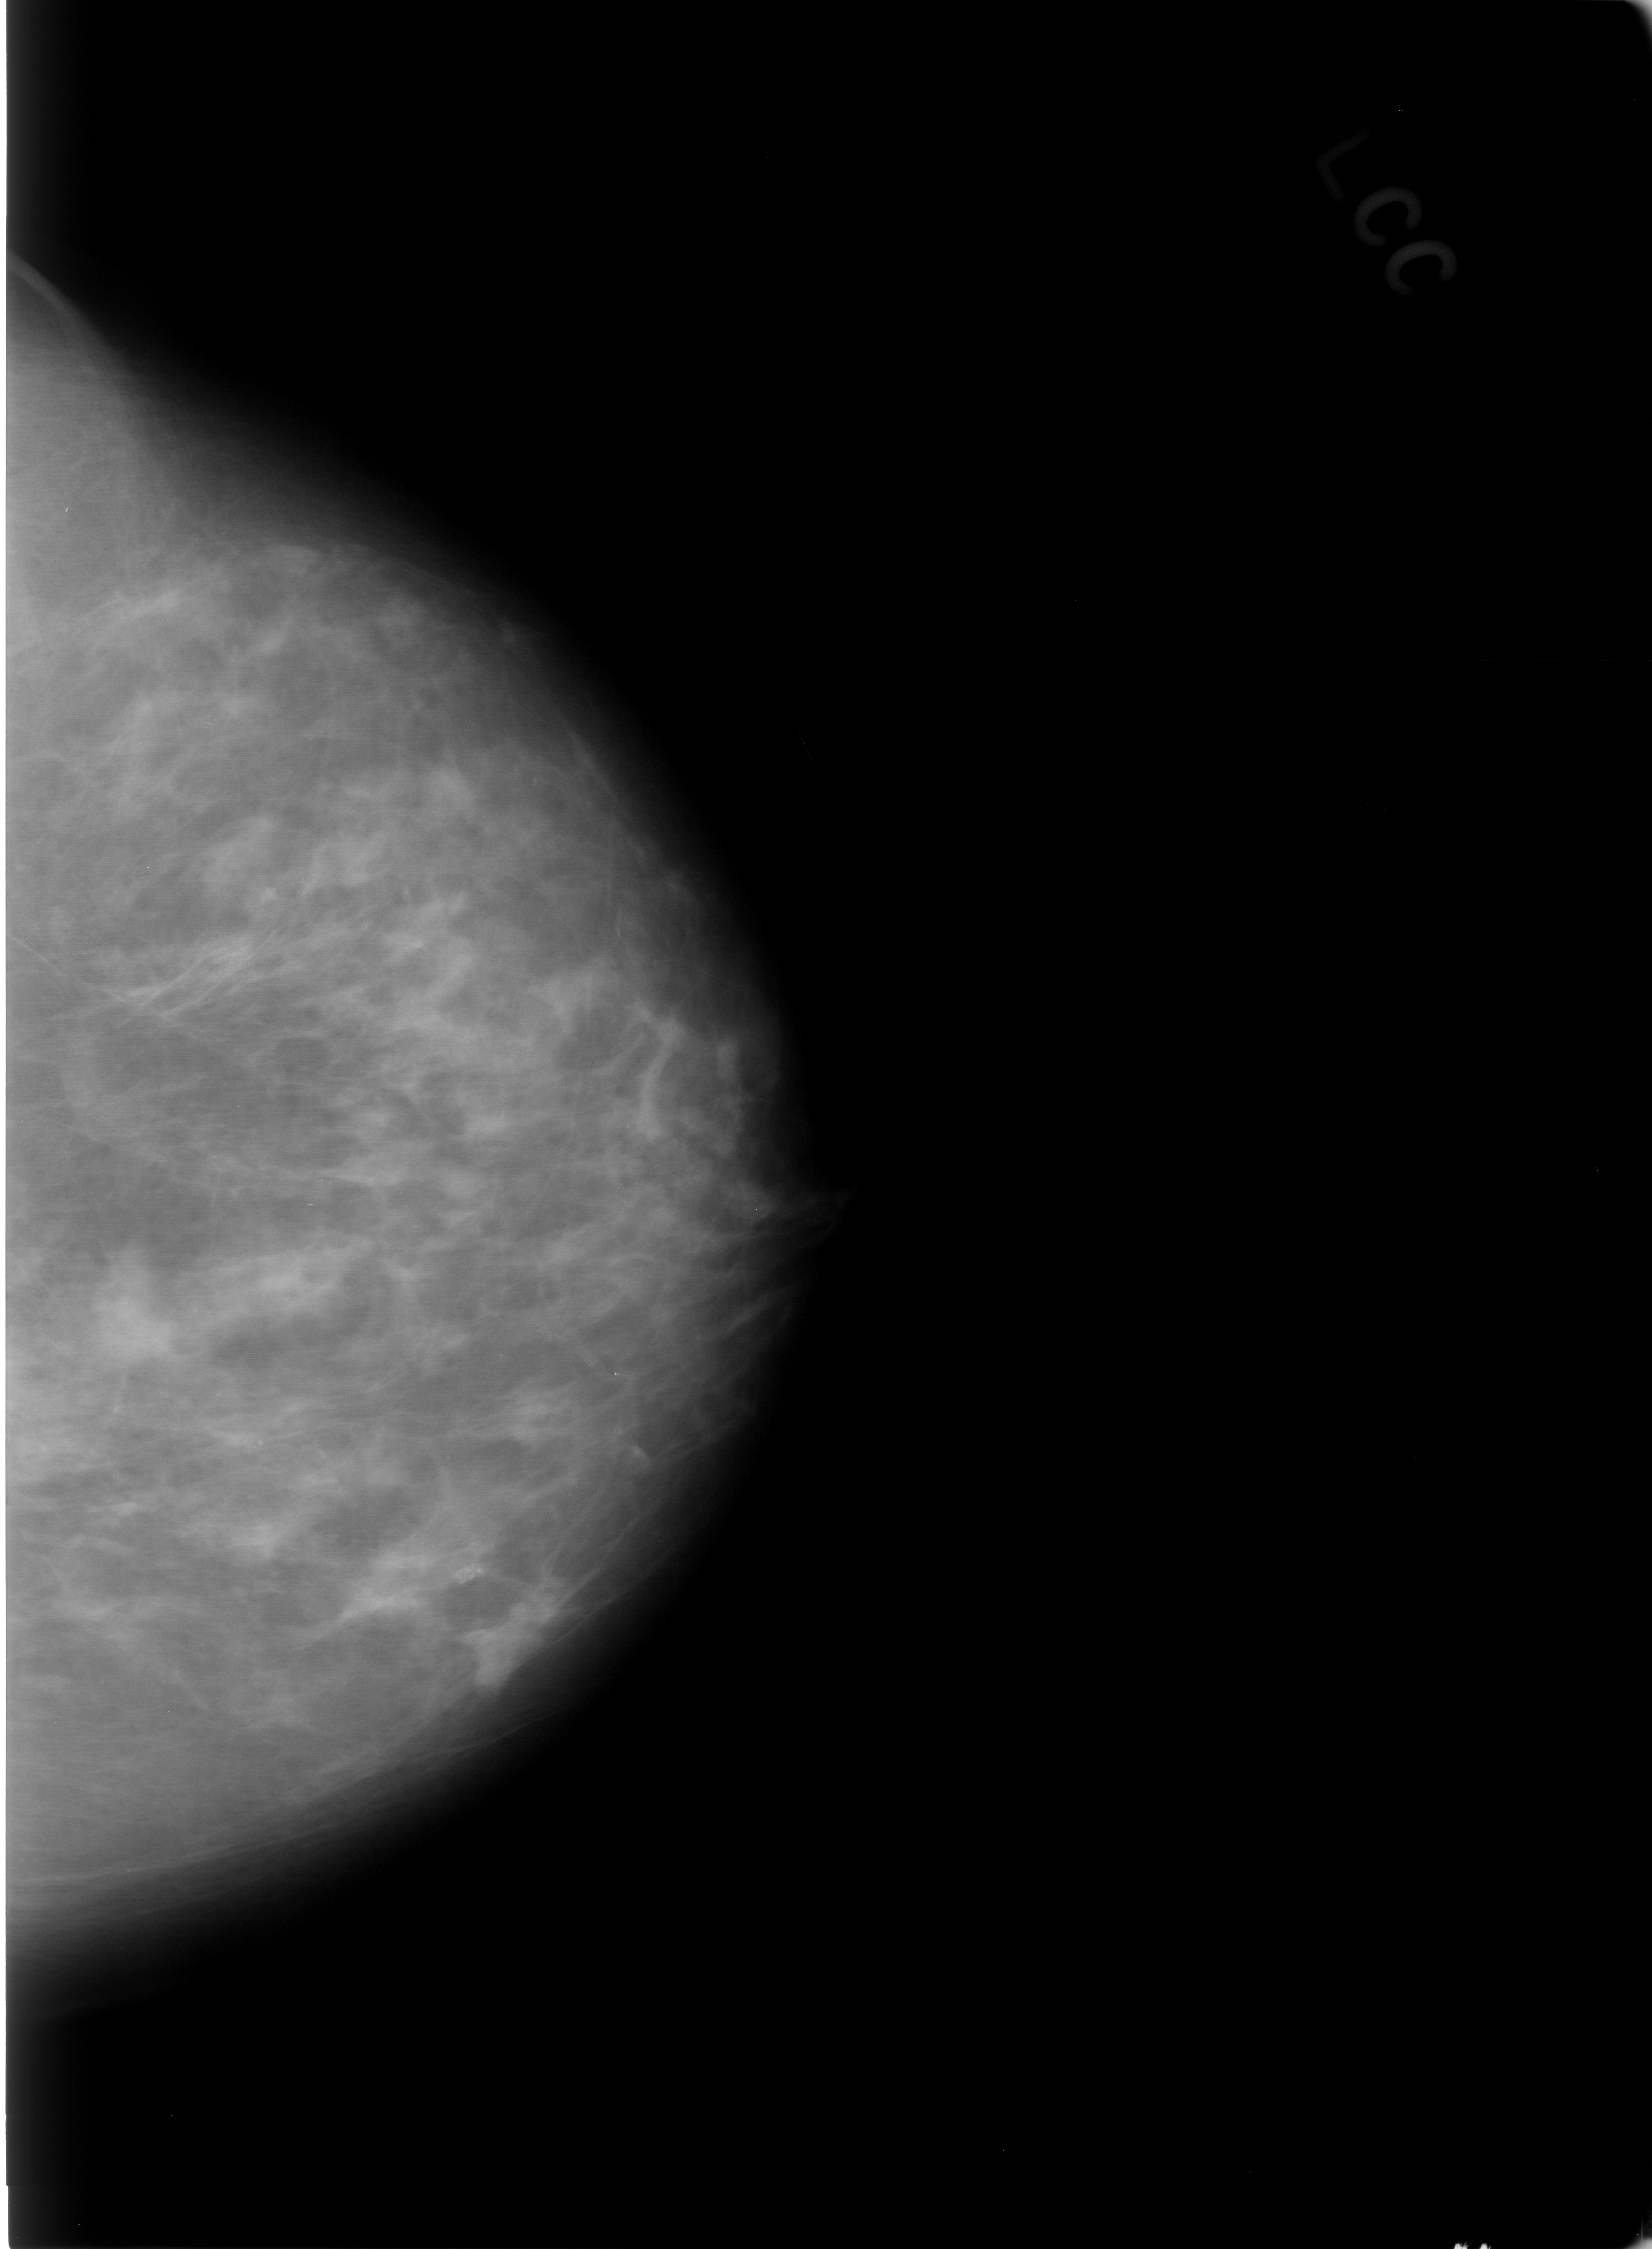
Digitized screen-film mammogram; left breast; CC view; breast composition: scattered fibroglandular densities (BI-RADS density category 2 of 4).
Abnormality record for this image: calcifications, morphology pleomorphic, distribution clustered; BI-RADS assessment category 4; pathology result (as recorded, not read from the image): benign.